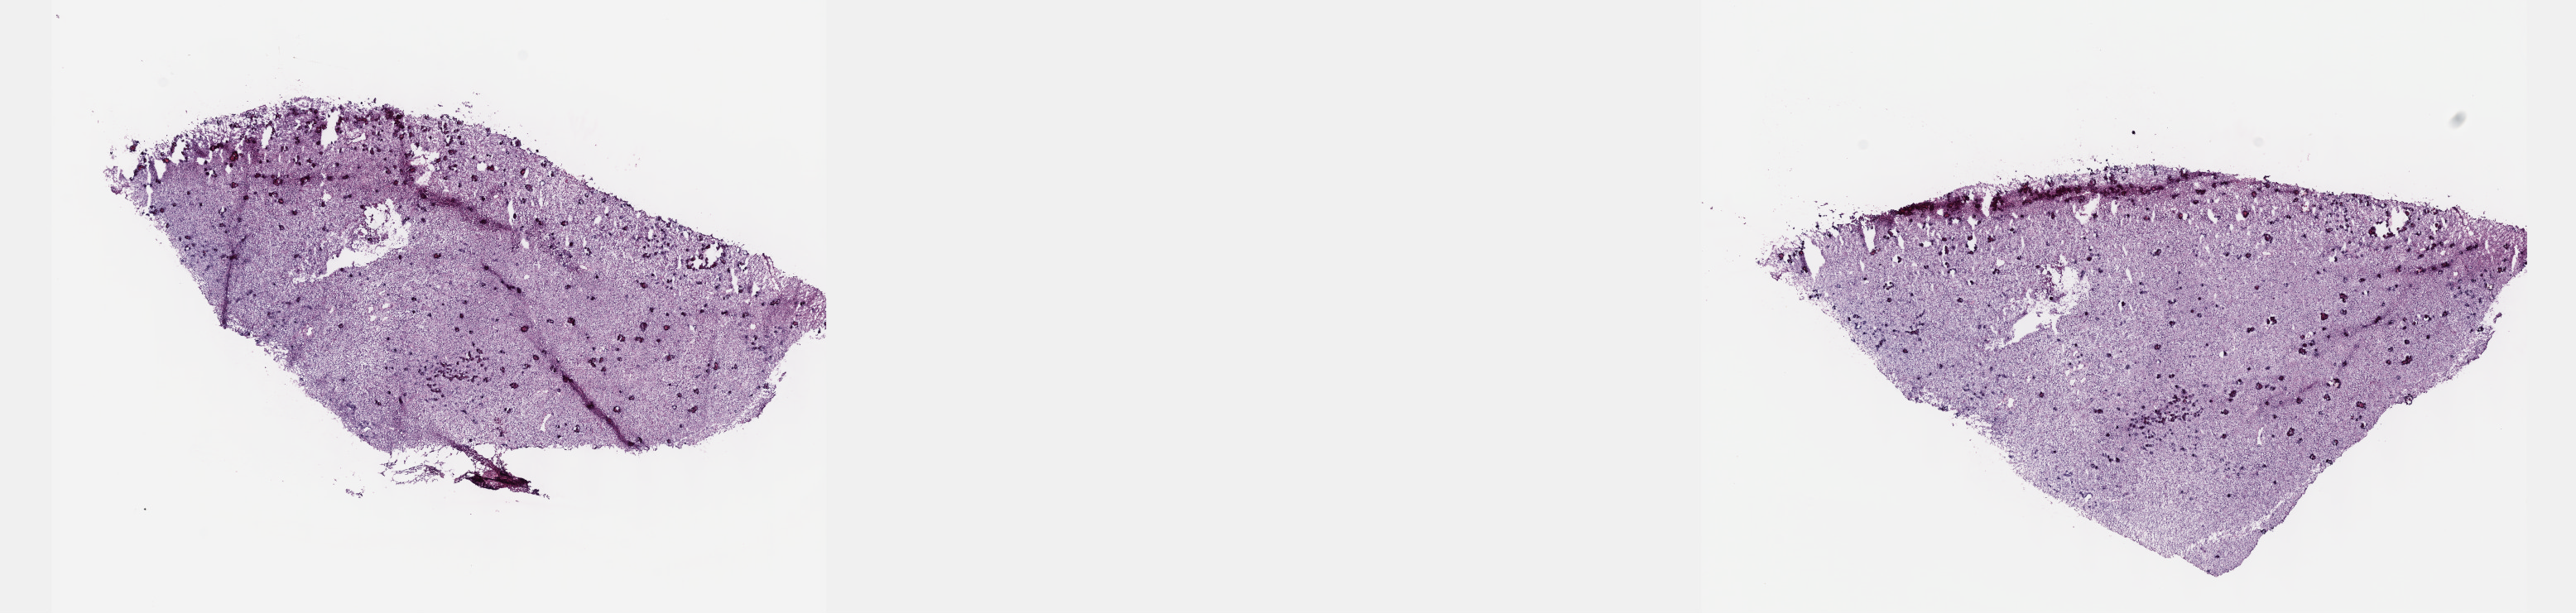
Digitized Hematoxylin and eosin (H&E) stained tissue section (whole slide), low-resolution overview of the scanned area, about 25.1 x 6.0 mm (from a 40x scan); frozen section from the top of the tissue portion; brain, recurrent tumour sample. Female patient; age at initial diagnosis 24 years. Pathologist review of this section (percent, as recorded): tumour cells 50%, tumour nuclei 90%, normal cells 25%, stromal cells 25%, necrosis 0%. Inflammatory infiltration, as recorded: lymphocyte infiltration 0%, monocyte infiltration 0%, neutrophil infiltration 0%.
This section: recurrent tumour. Patient diagnosis: Oligodendroglioma, anaplastic (cerebrum).